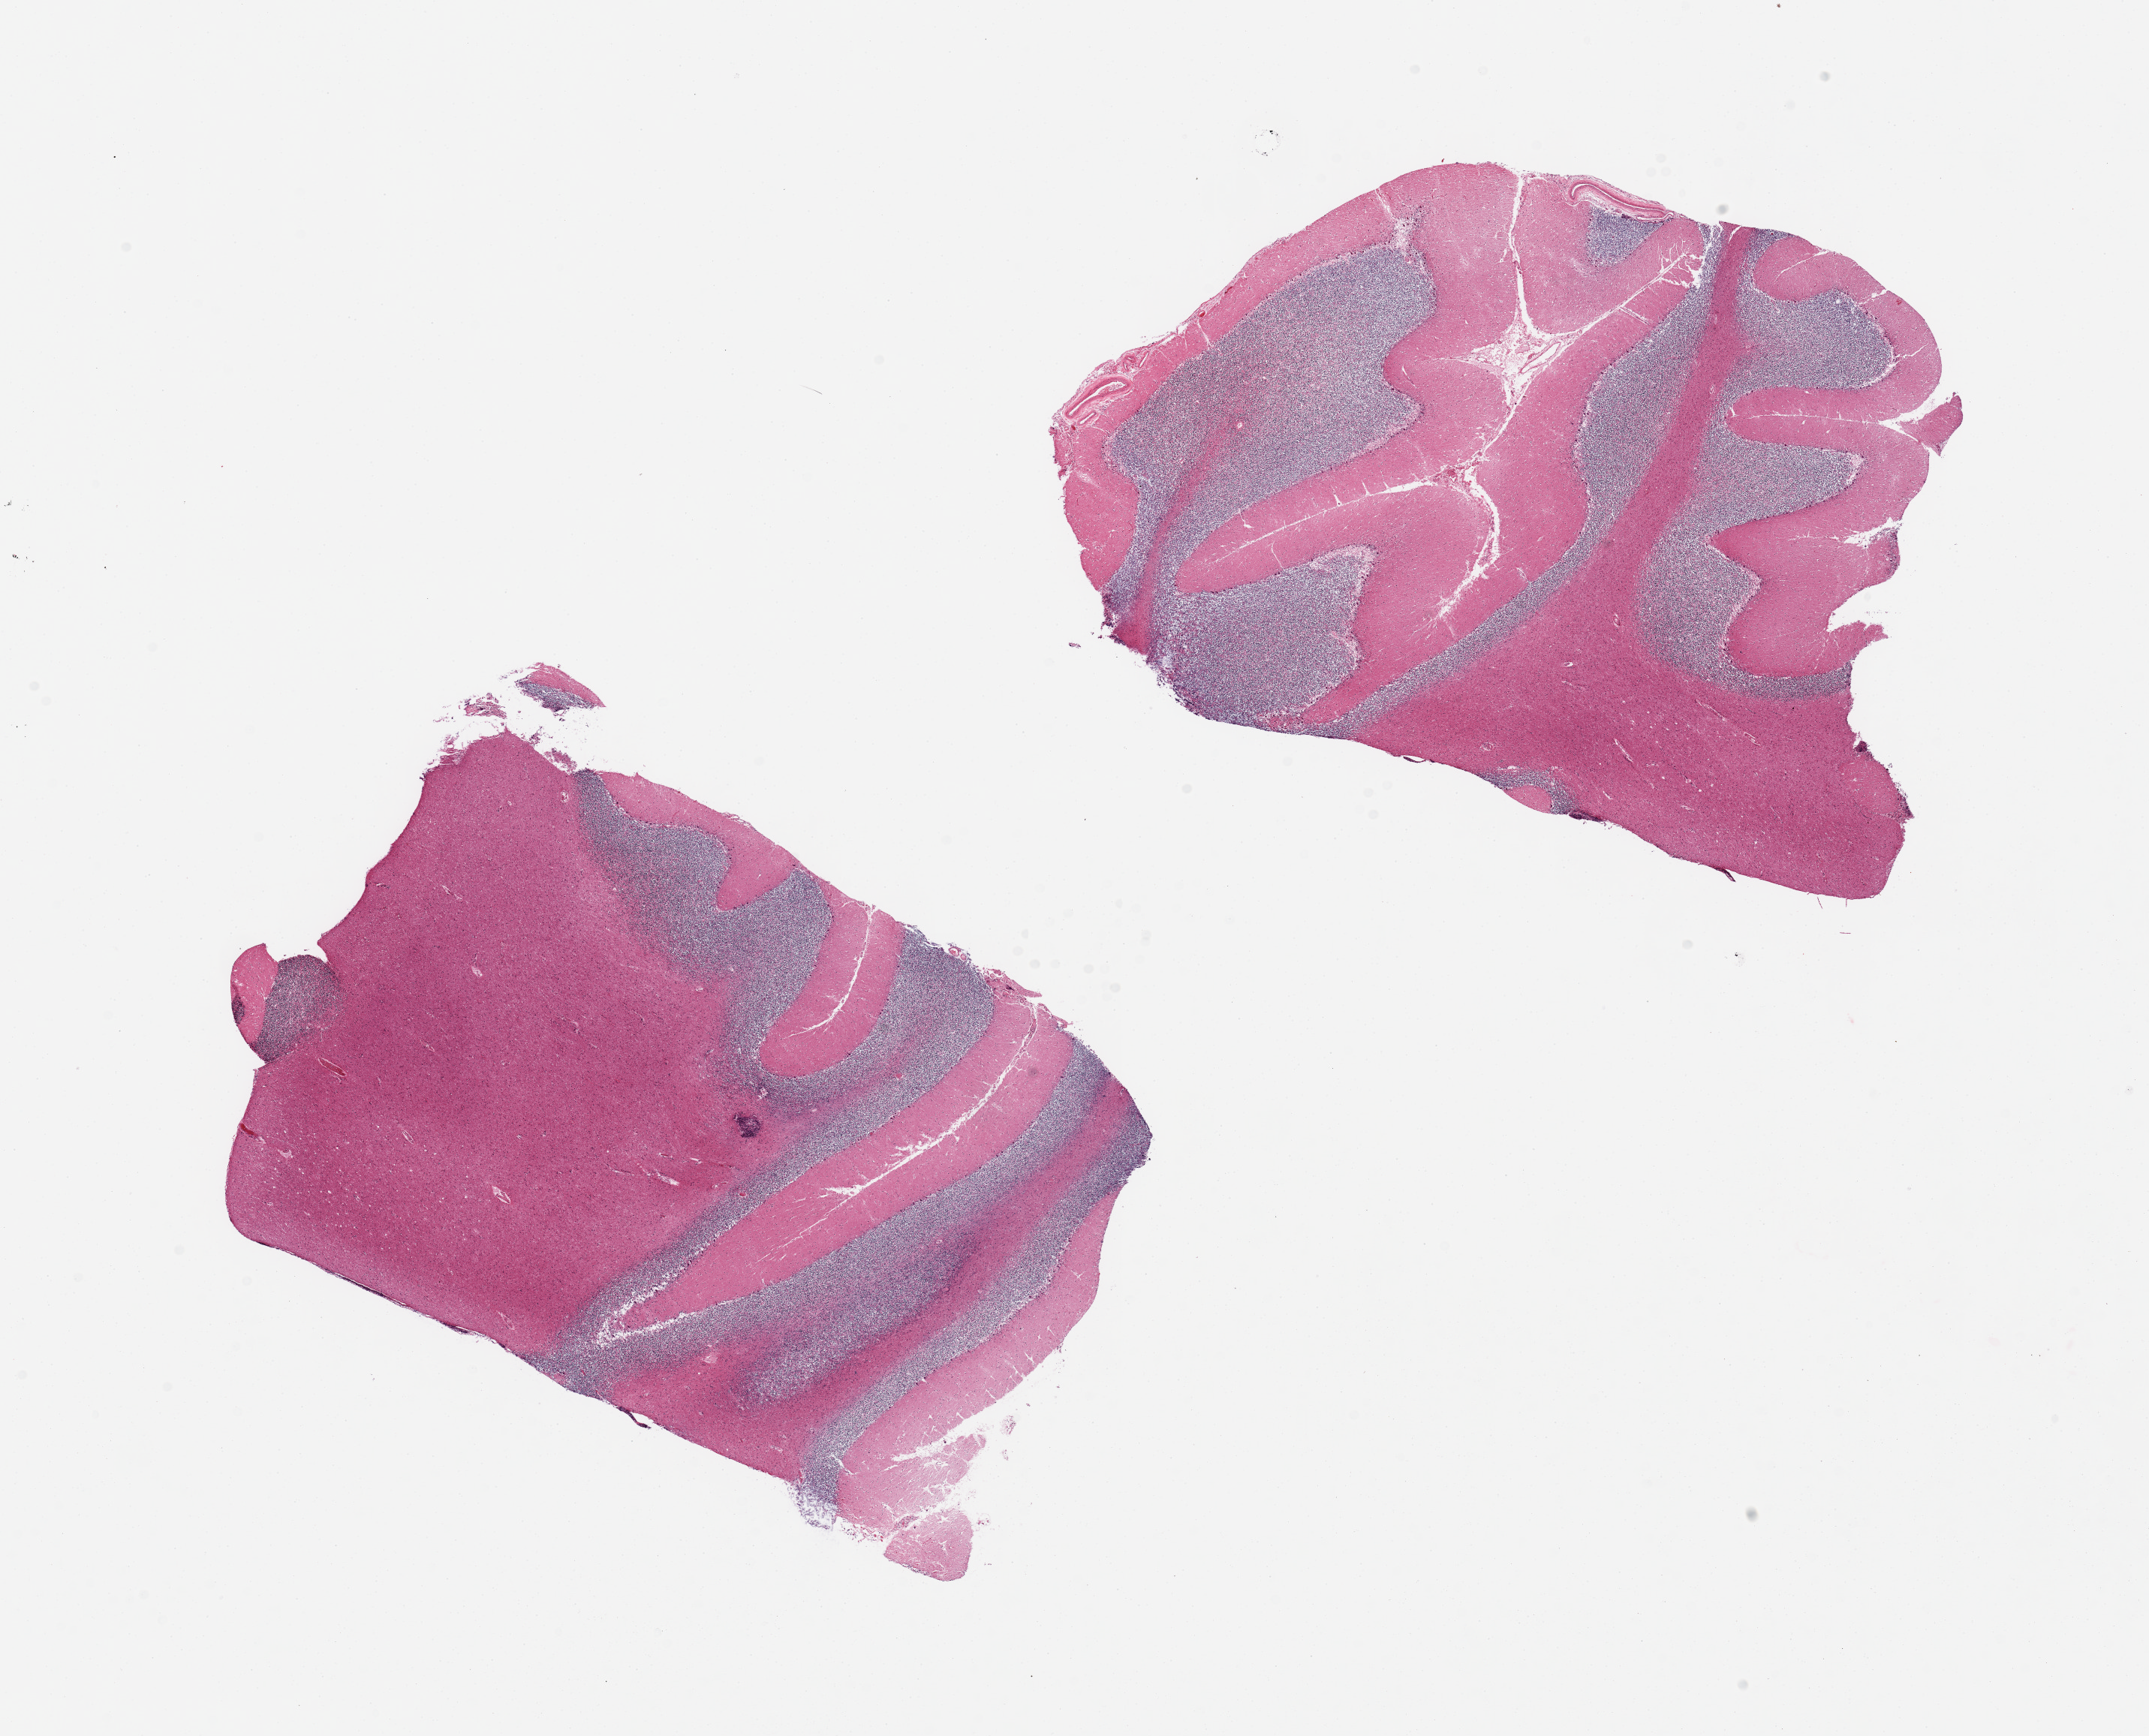
Digitized hematoxylin and eosin (H&E)-stained section — low-resolution overview of the scanned area, about 22.6 x 18.3 mm (acquisition: 20x scan). PAXgene-fixed, paraffin-embedded tissue. Sampled site (target tissue): cerebellum. Tissue donor sample. Donor sex: male.
Review note (as recorded): 2 pieces Purkinje cells visualized; evidence of antemortem hypoxia.